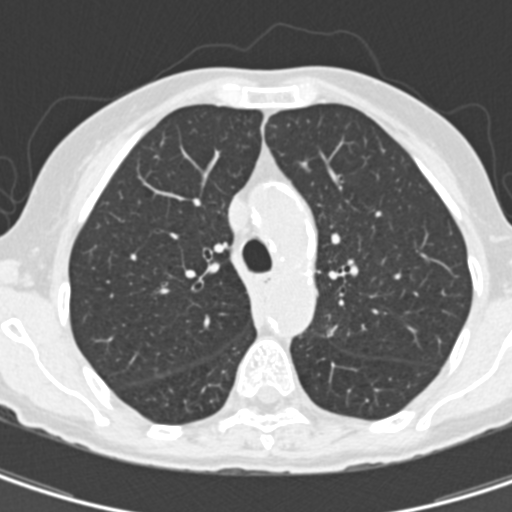
Chest CT (low-dose screening protocol), one axial image, first (baseline) screen, lung window (W 1500 / L -600 HU), 120 kVp, slice 51 of 157 in the series. Female participant, aged 67 years at enrolment. Current smoker at enrolment.
Expert-annotated lung lesion, bounding box <315,312,360,359> (left, top, right, bottom; pixels). Screening reader's record for this exam (one nodule recorded; not confirmed to be the boxed lesion): non-calcified nodule or mass ≥4 mm, left upper lobe, 11 × 8 mm, spiculated (stellate) margins, soft tissue attenuation. Lung cancer was diagnosed 73 days after this screen: adenocarcinoma, NOS, left upper lobe, poorly differentiated (G3), stage IA (AJCC 6th edition), 13 mm at pathology.